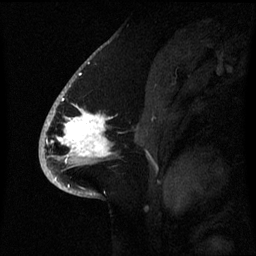
Breast MRI (dynamic contrast-enhanced), one sagittal slice; slice 39 of 60 in the series (ordered by position); dynamic contrast-enhanced series, image 2 of 3 at this slice position (ordered by acquisition); 1.5 T; TE 4.2 ms, TR 8.4 ms; 256 × 256 image matrix, field of view 220 × 220 mm. Female patient, age 53 years. From the clinical record (not read from this slice): setting: breast cancer imaged before/during neoadjuvant chemotherapy; receptor status: HR-positive, HER2-negative.
Outlined on this slice (semi-automatic segmentation, software-assisted and operator-edited):
- analysis volume of interest (the breast-tissue region the enhancement analysis was run in; not a lesion): bounding box [x1, y1, x2, y2] px = [52, 90, 115, 171]
- tumour enhancement mask (voxels above the 70 % enhancement threshold inside the analysis volume of interest): [58, 112, 112, 161]